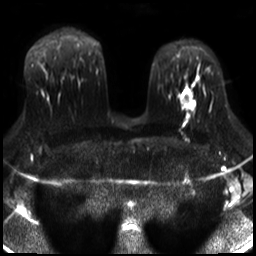
Breast MRI, one axial slice. Diffusion-weighted series; image 2 of 4 stored at this slice position (different b-values; order by instance number). 3 T. 256 × 256 image matrix, field of view 320 × 320 mm. Female patient.
Annotated regions visible in this slice (expert manual segmentation):
- tumour on diffusion-weighted imaging: bounding box (x1, y1, x2, y2) in pixels: (180, 96, 193, 110)